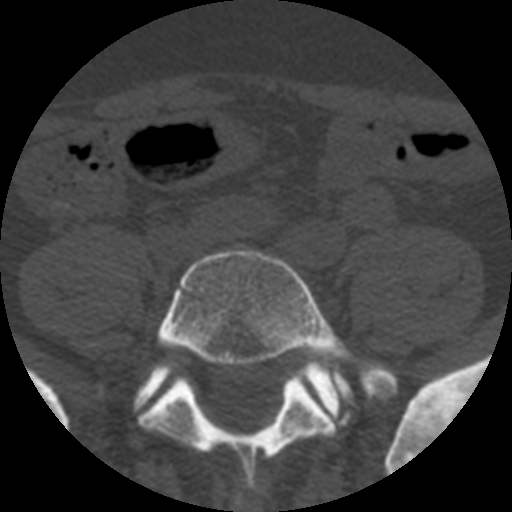
CT including the spine, one axial slice; position 61 of 508 along the scan axis; 120 kVp; bone window (W 1800 / L 400 HU); 1.25 mm slice thickness; 512 × 512 image matrix. Patient age 57 years. Case-level facts recorded for this patient, not image findings: primary cancer: prostate.
Outlined on this slice (semi-automatically segmented with operator editing):
- L5 vertebra: bounding box (x1, y1, x2, y2) in pixels: (140, 250, 394, 490)